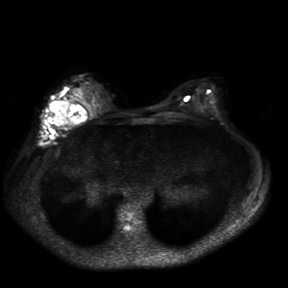
Breast MRI, one axial slice; slice 18 of 30 in the series (ordered by position); diffusion-weighted series; image 2 of 4 stored at this slice position (different b-values; order by instance number); 3 T; 4 mm slice thickness; 288 × 288 image matrix, field of view 360 × 360 mm. Female patient.
Annotated regions visible in this slice (manually delineated by an expert):
- tumour on diffusion-weighted imaging: bounding box (x1, y1, x2, y2) in pixels: (53, 101, 72, 124)